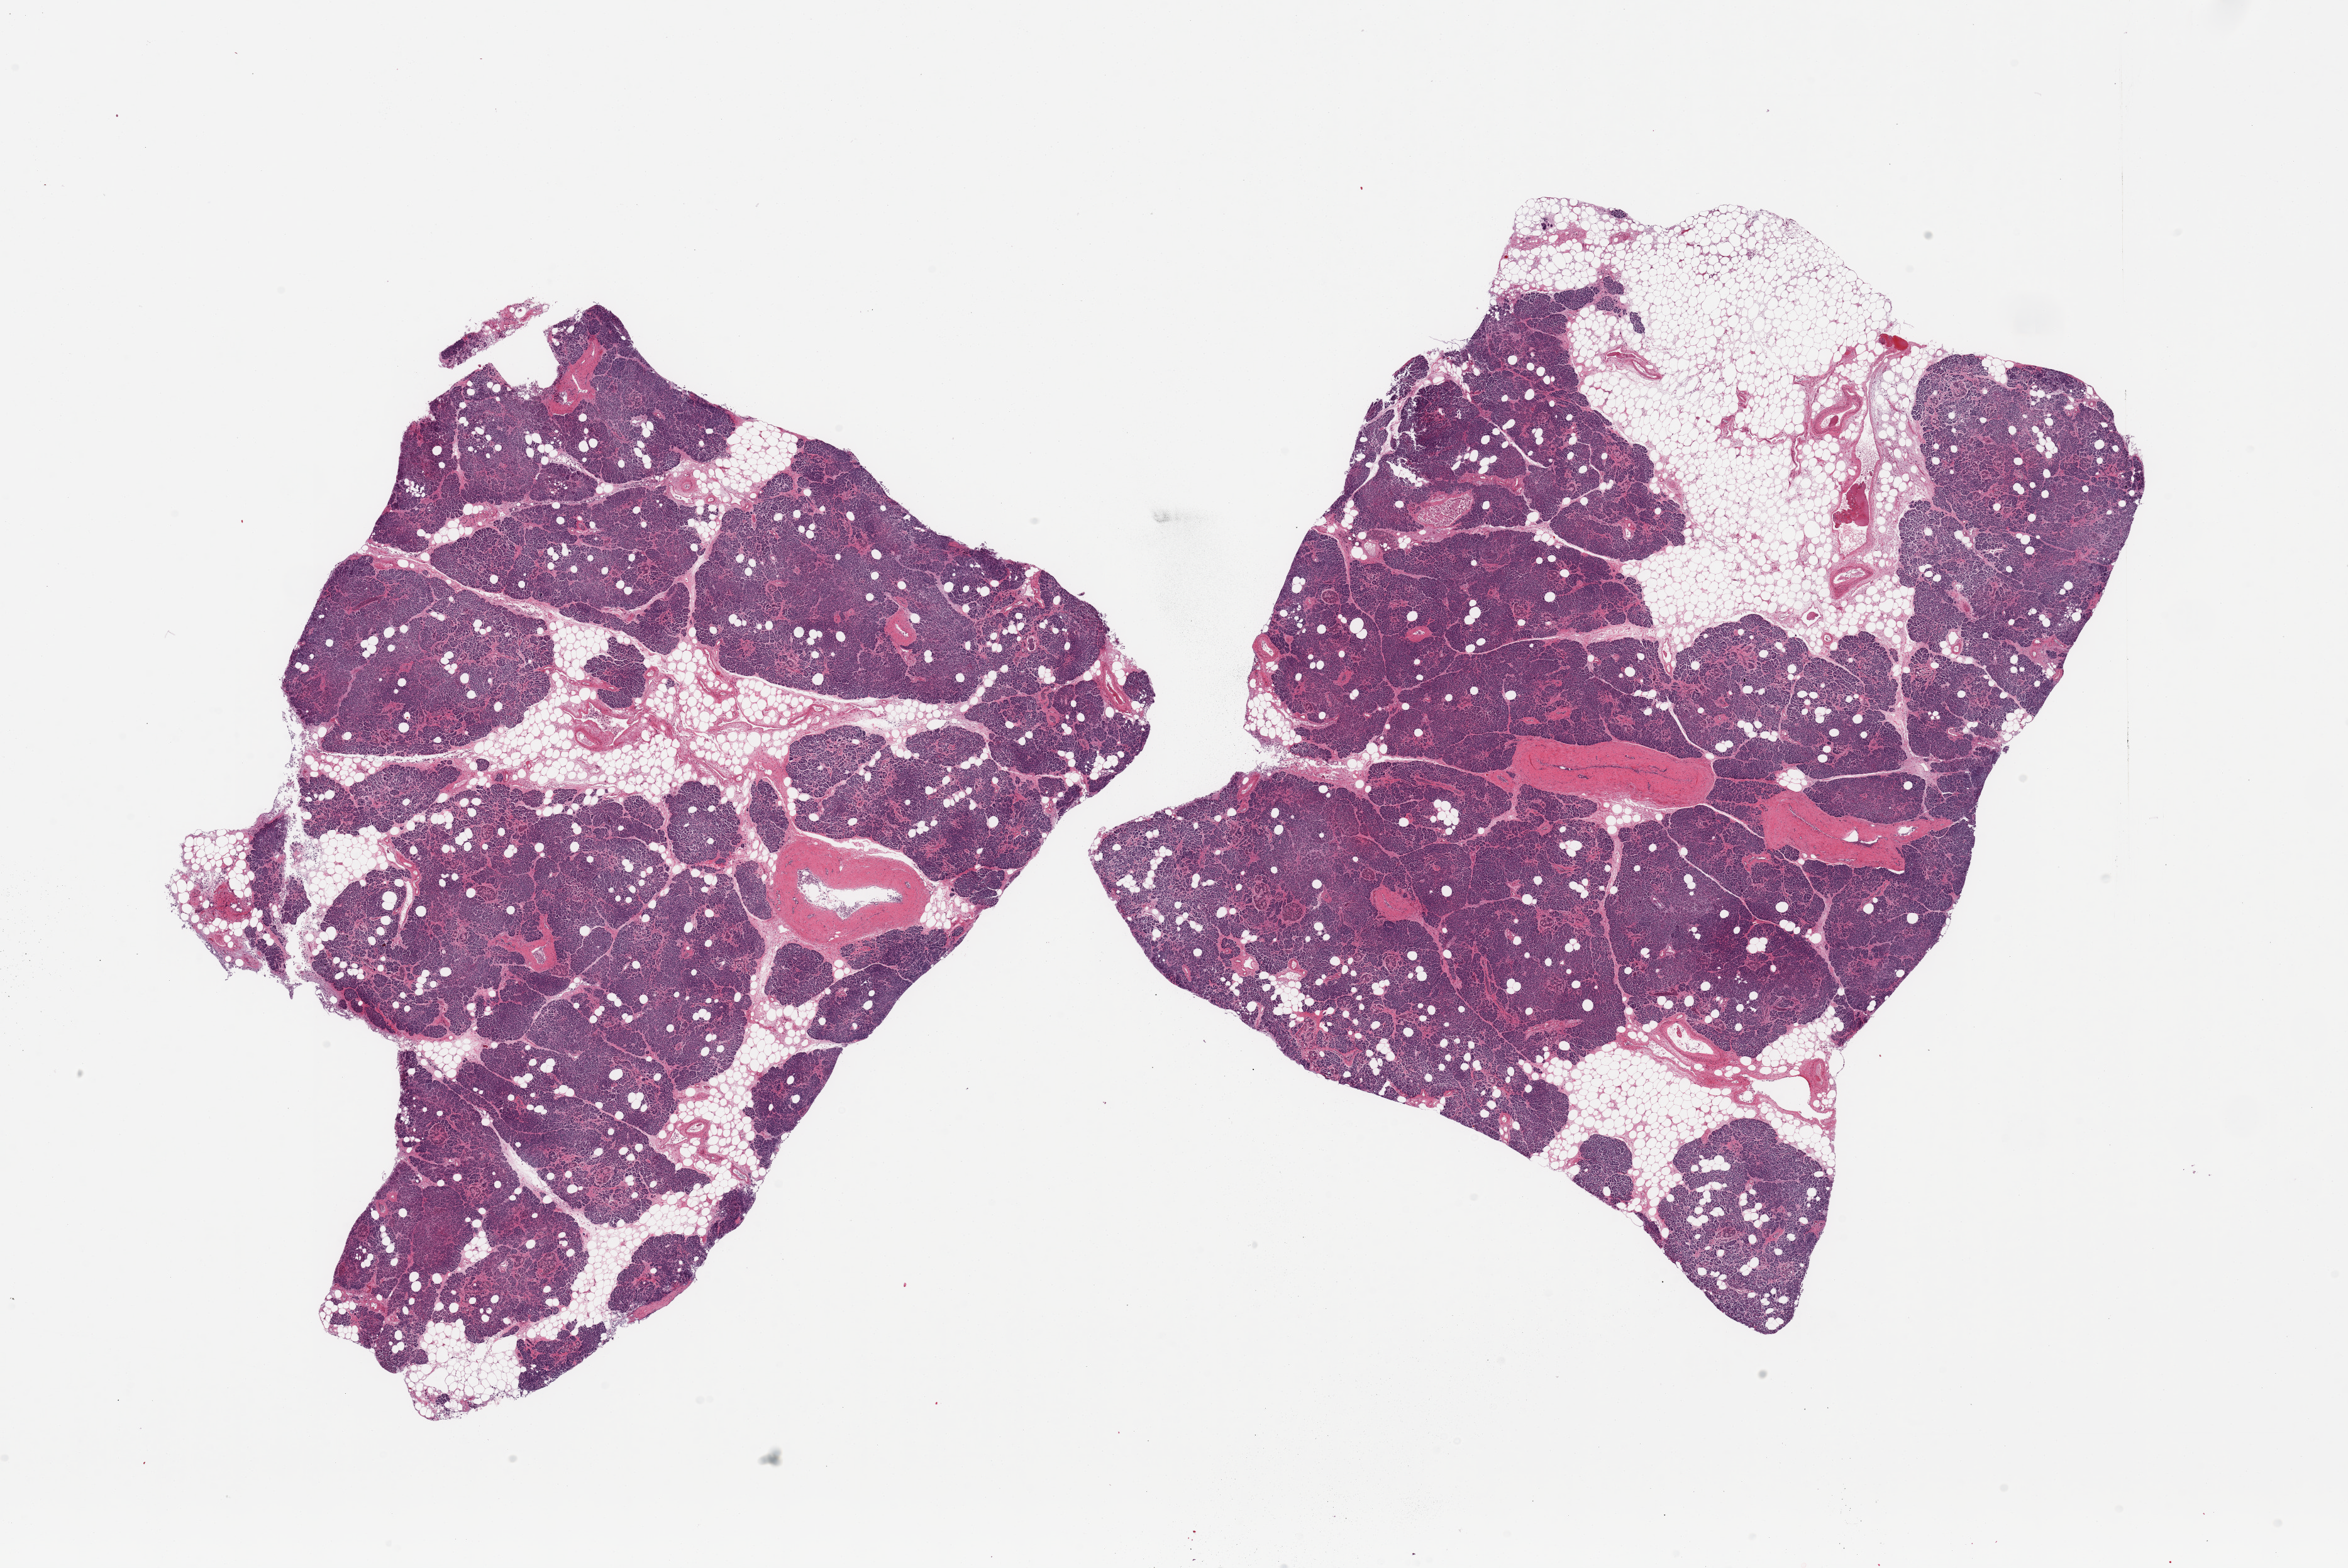
H&E whole-slide image, brightfield — shown as a low-resolution overview of the whole scanned area (about 29.5 x 19.7 mm); PAXgene-fixed paraffin-embedded (PFPE) section; target tissue: pancreas; donor tissue sample. Donor sex: male.
Reviewer comment on this tissue sample: 2 pieces, moderately advanced saponificiation, few Islets visible, laregely degenerated, rep dencircled.